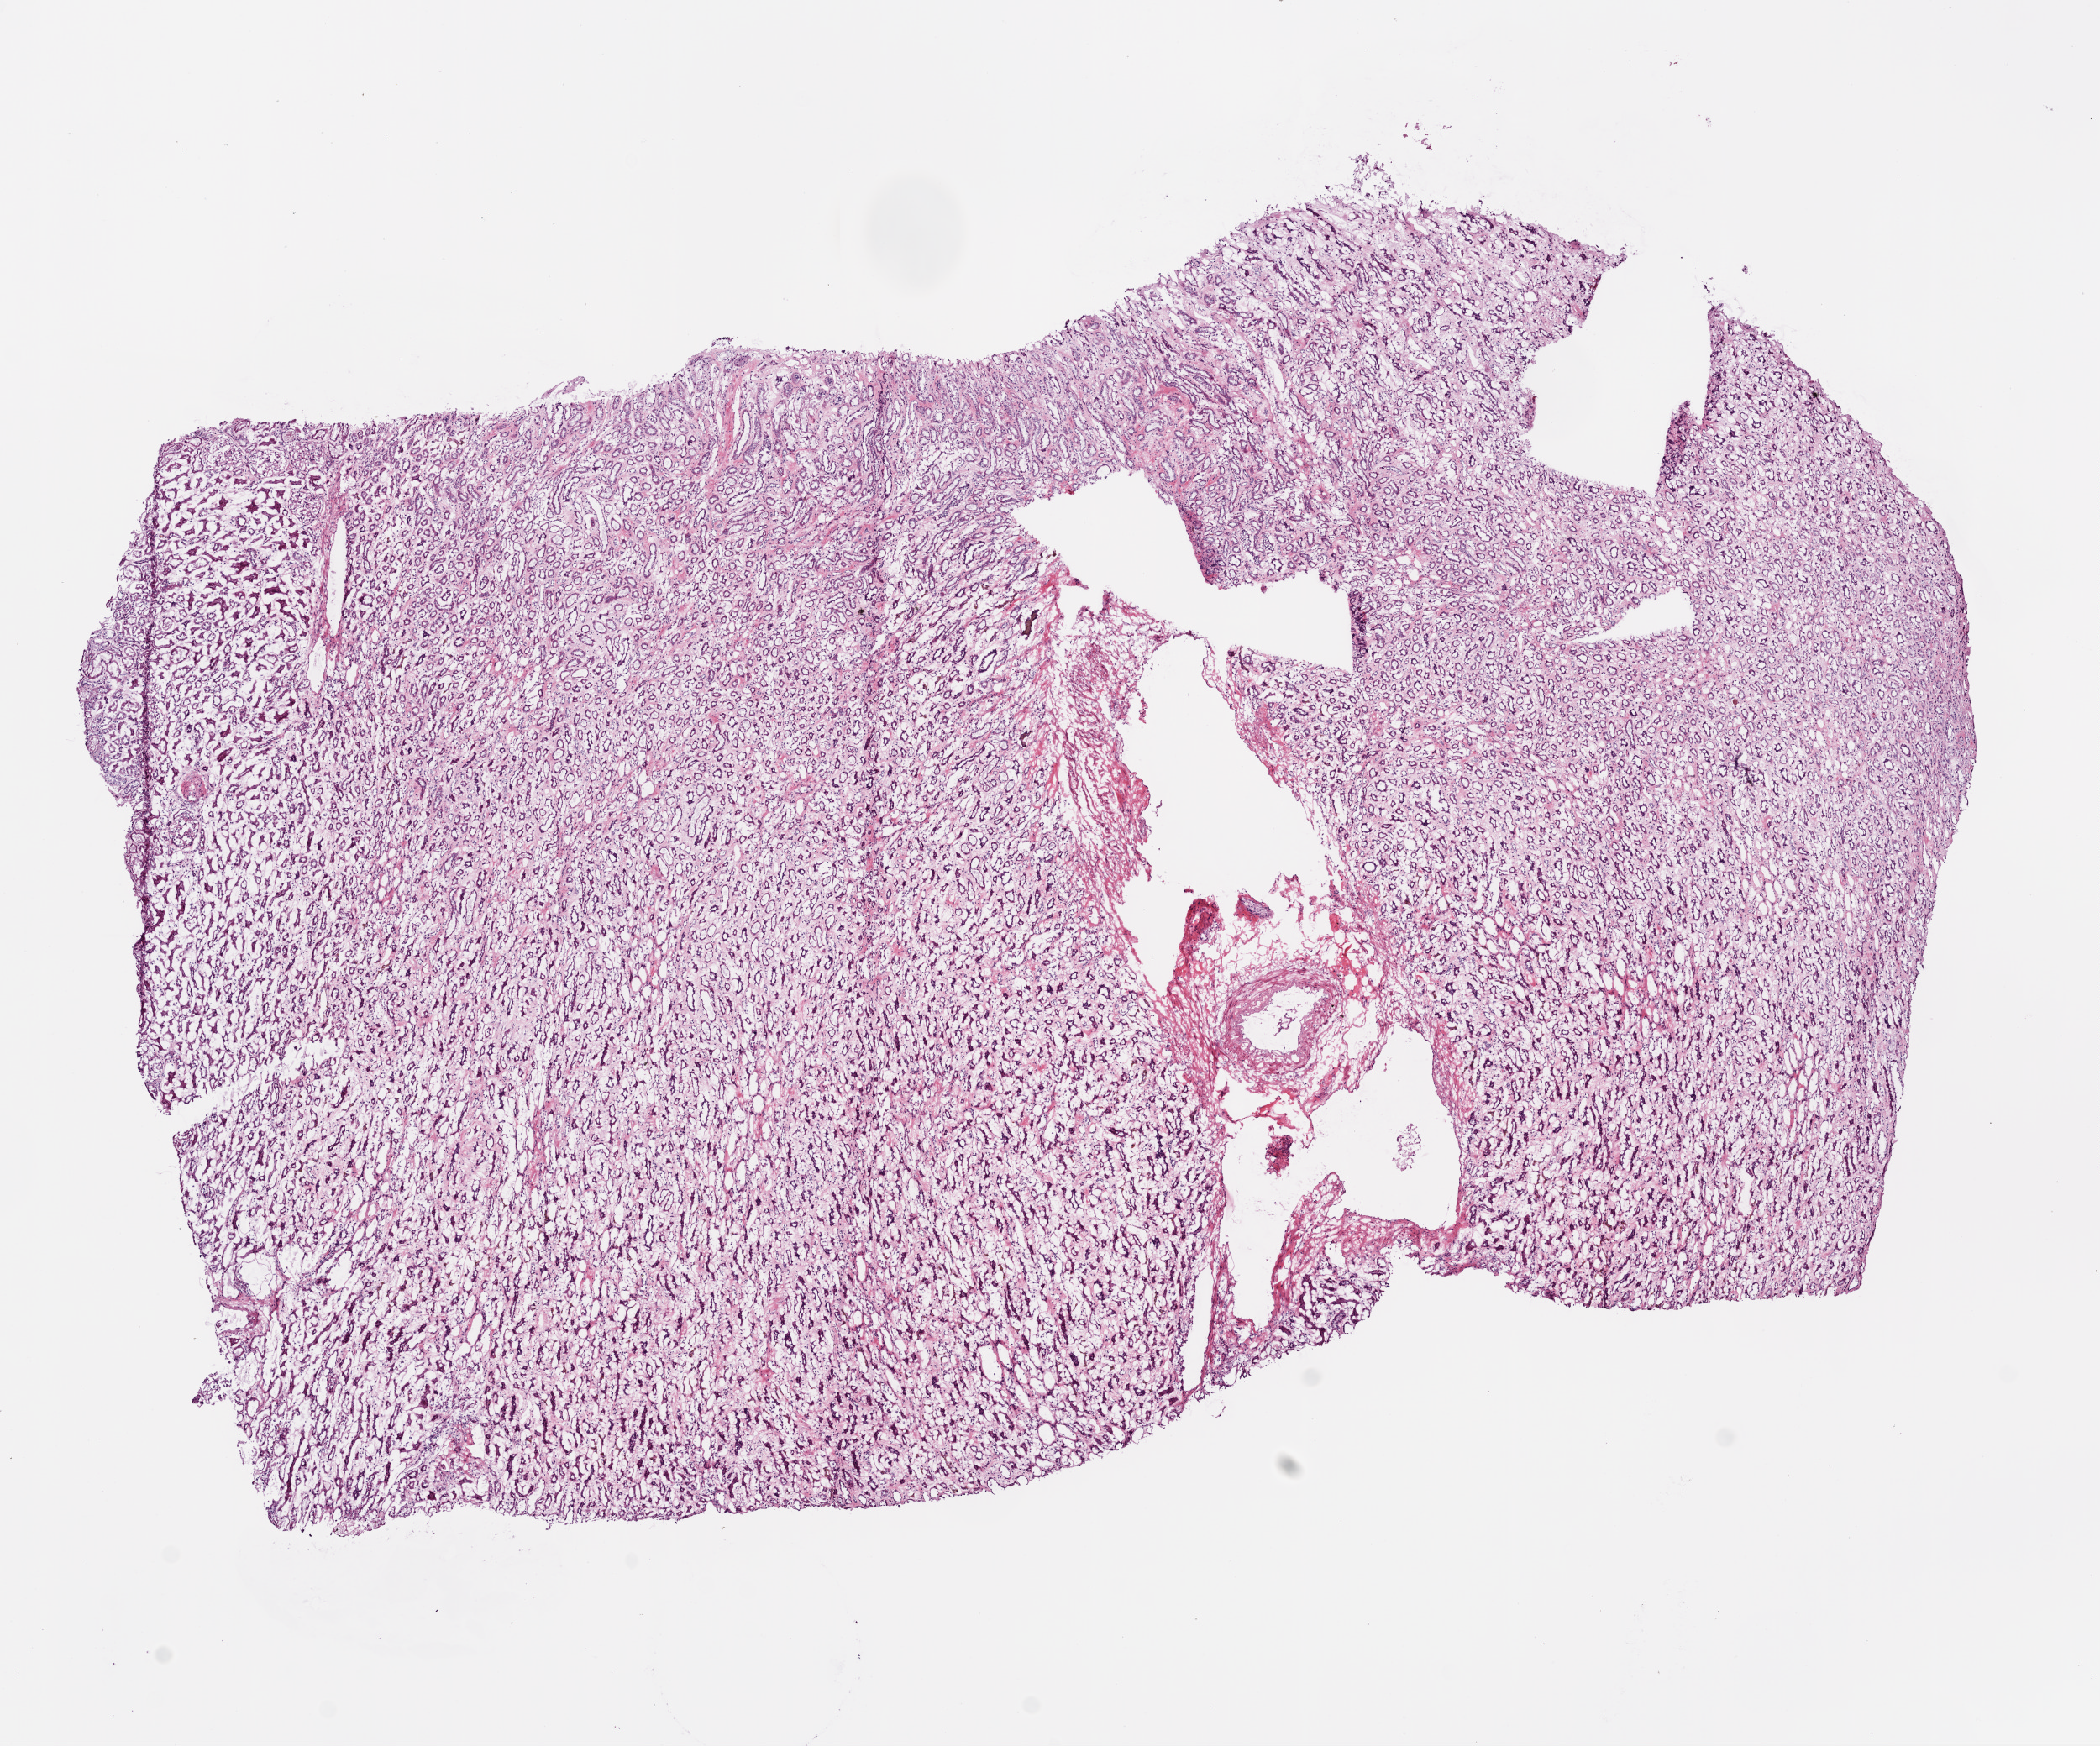
Whole-slide histology image, H&E, low-resolution overview of the scanned area, about 10.0 x 8.3 mm (acquisition: 20x scan); frozen section from the bottom of the tissue portion; solid tissue normal (non-tumour tissue) sample from the kidney. Patient: female, age at initial diagnosis 59 years.
* this section: solid tissue normal (non-tumour) sample from the same patient
* patient diagnosis: Clear cell adenocarcinoma, NOS